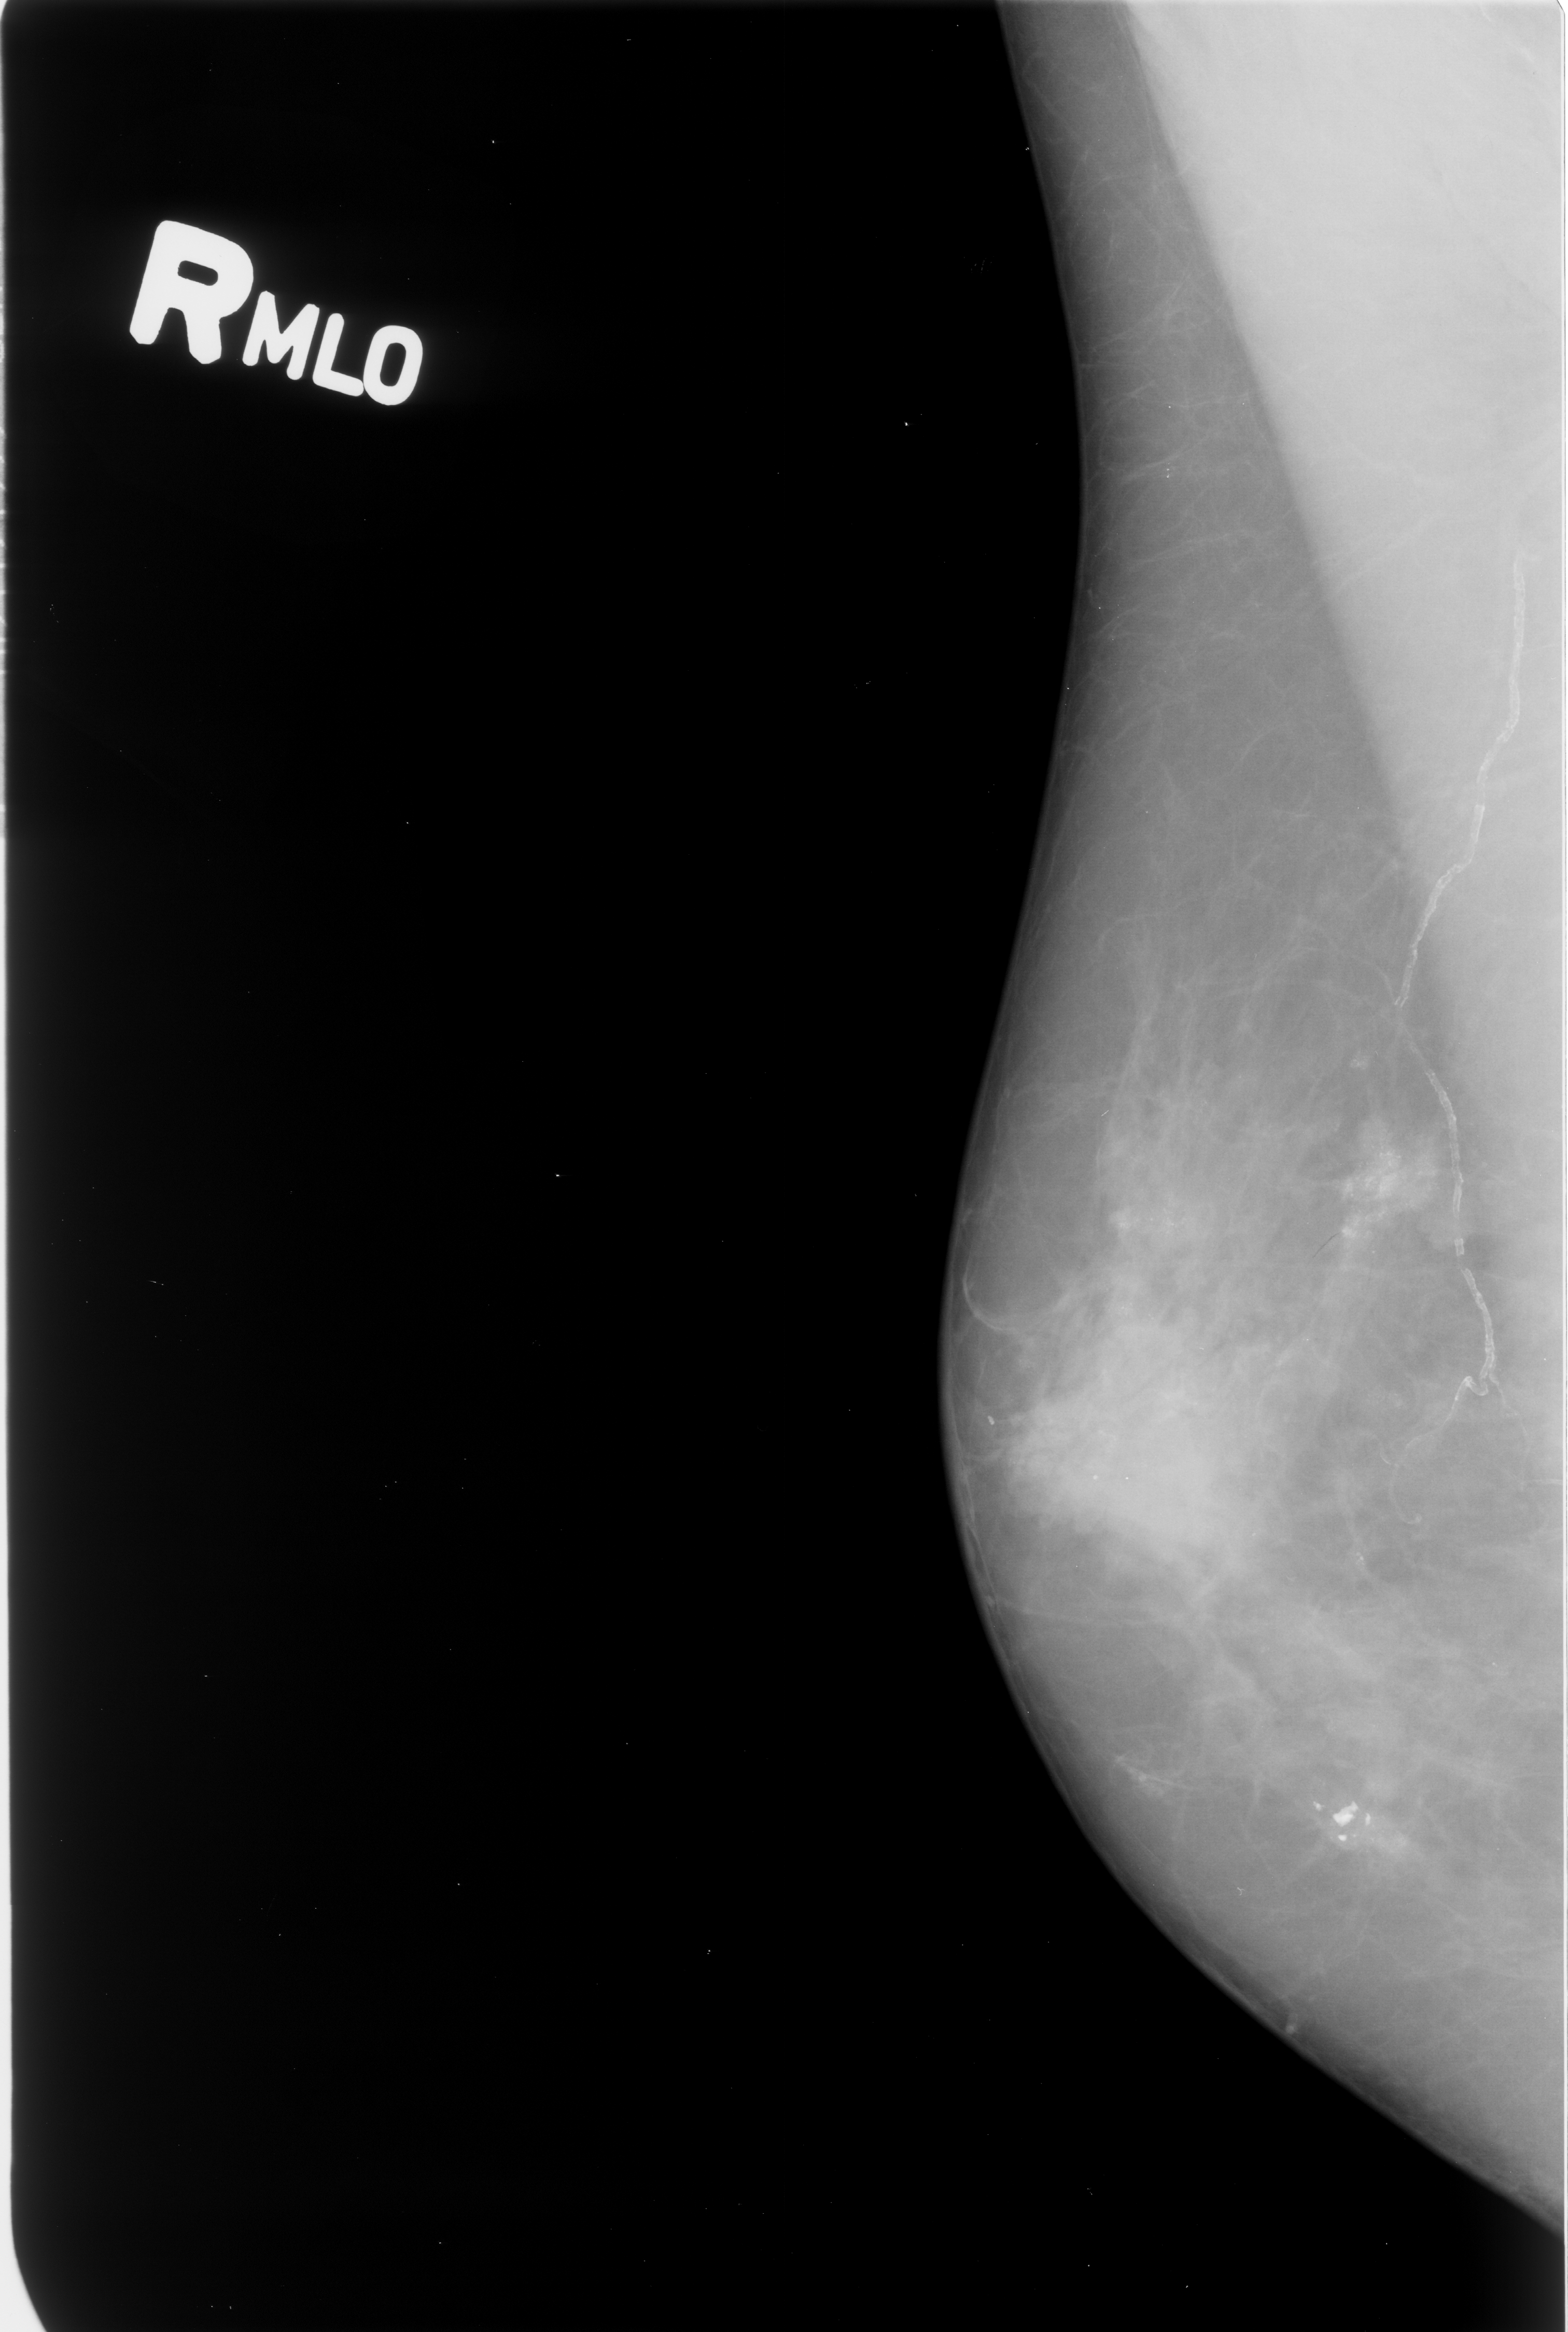
Mammogram (digitized film), right breast, mediolateral oblique (MLO) view, BI-RADS breast density category 3 (scale 1–4).
Finding: calcifications, morphology punctate / pleomorphic, distribution clustered; BI-RADS assessment category 4; subtlety rating 3 on a 1 (subtle) to 5 (obvious) scale; pathology (as recorded): malignant.